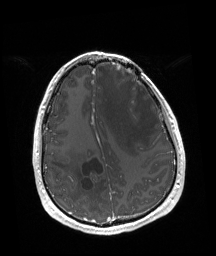
Brain MRI from a brain-tumour surgery series, one axial slice. Position 56 of 192 along the scan axis. T1-weighted post-contrast. 1 mm slice thickness. 216 × 256 image matrix, field of view 219 × 260 mm.
Structures marked on this image (manually delineated by an expert):
- tumour: bounding box <125,68,136,76> (left, top, right, bottom; pixels)